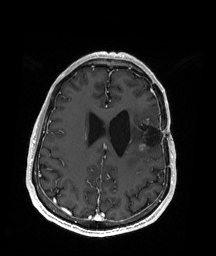
Brain MRI from a brain-tumour surgery series, one axial slice. Position 68 of 192 along the scan axis. T1-weighted post-contrast. 216 × 256 image matrix, field of view 211 × 250 mm. From the clinical record (not read from this slice): histopathology: Oligodendroglioma; WHO grade: 2; IDH mutation: yes.
Annotated regions visible in this slice (outlined manually by an expert reader):
- previous resection cavity: bounding box [x1, y1, x2, y2] px = [132, 121, 163, 146]
- tumour: [139, 117, 150, 152]